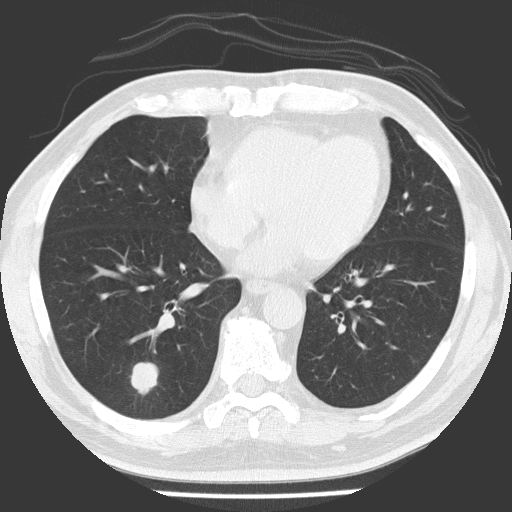
Low-dose screening chest CT, axial slice; first (baseline) screen; lung window (W 1500 / L -600 HU); 2 mm slice thickness; slice 92 of 154 in the series. Male participant, aged 56 years at enrolment. Former smoker at enrolment.
• Expert reader's lesion annotation, bounding box <112,348,166,404> (left, top, right, bottom; pixels).
• Reader record for this screening exam (exam-level; its link to the box is not recorded): non-calcified nodule or mass ≥4 mm, right lower lobe, 21 × 17 mm, spiculated (stellate) margins, soft tissue attenuation.
• Lung cancer was diagnosed 84 days after this screen: adenocarcinoma, NOS, right lower lobe, poorly differentiated (G3), stage IA (AJCC 6th edition), 24 mm at pathology.